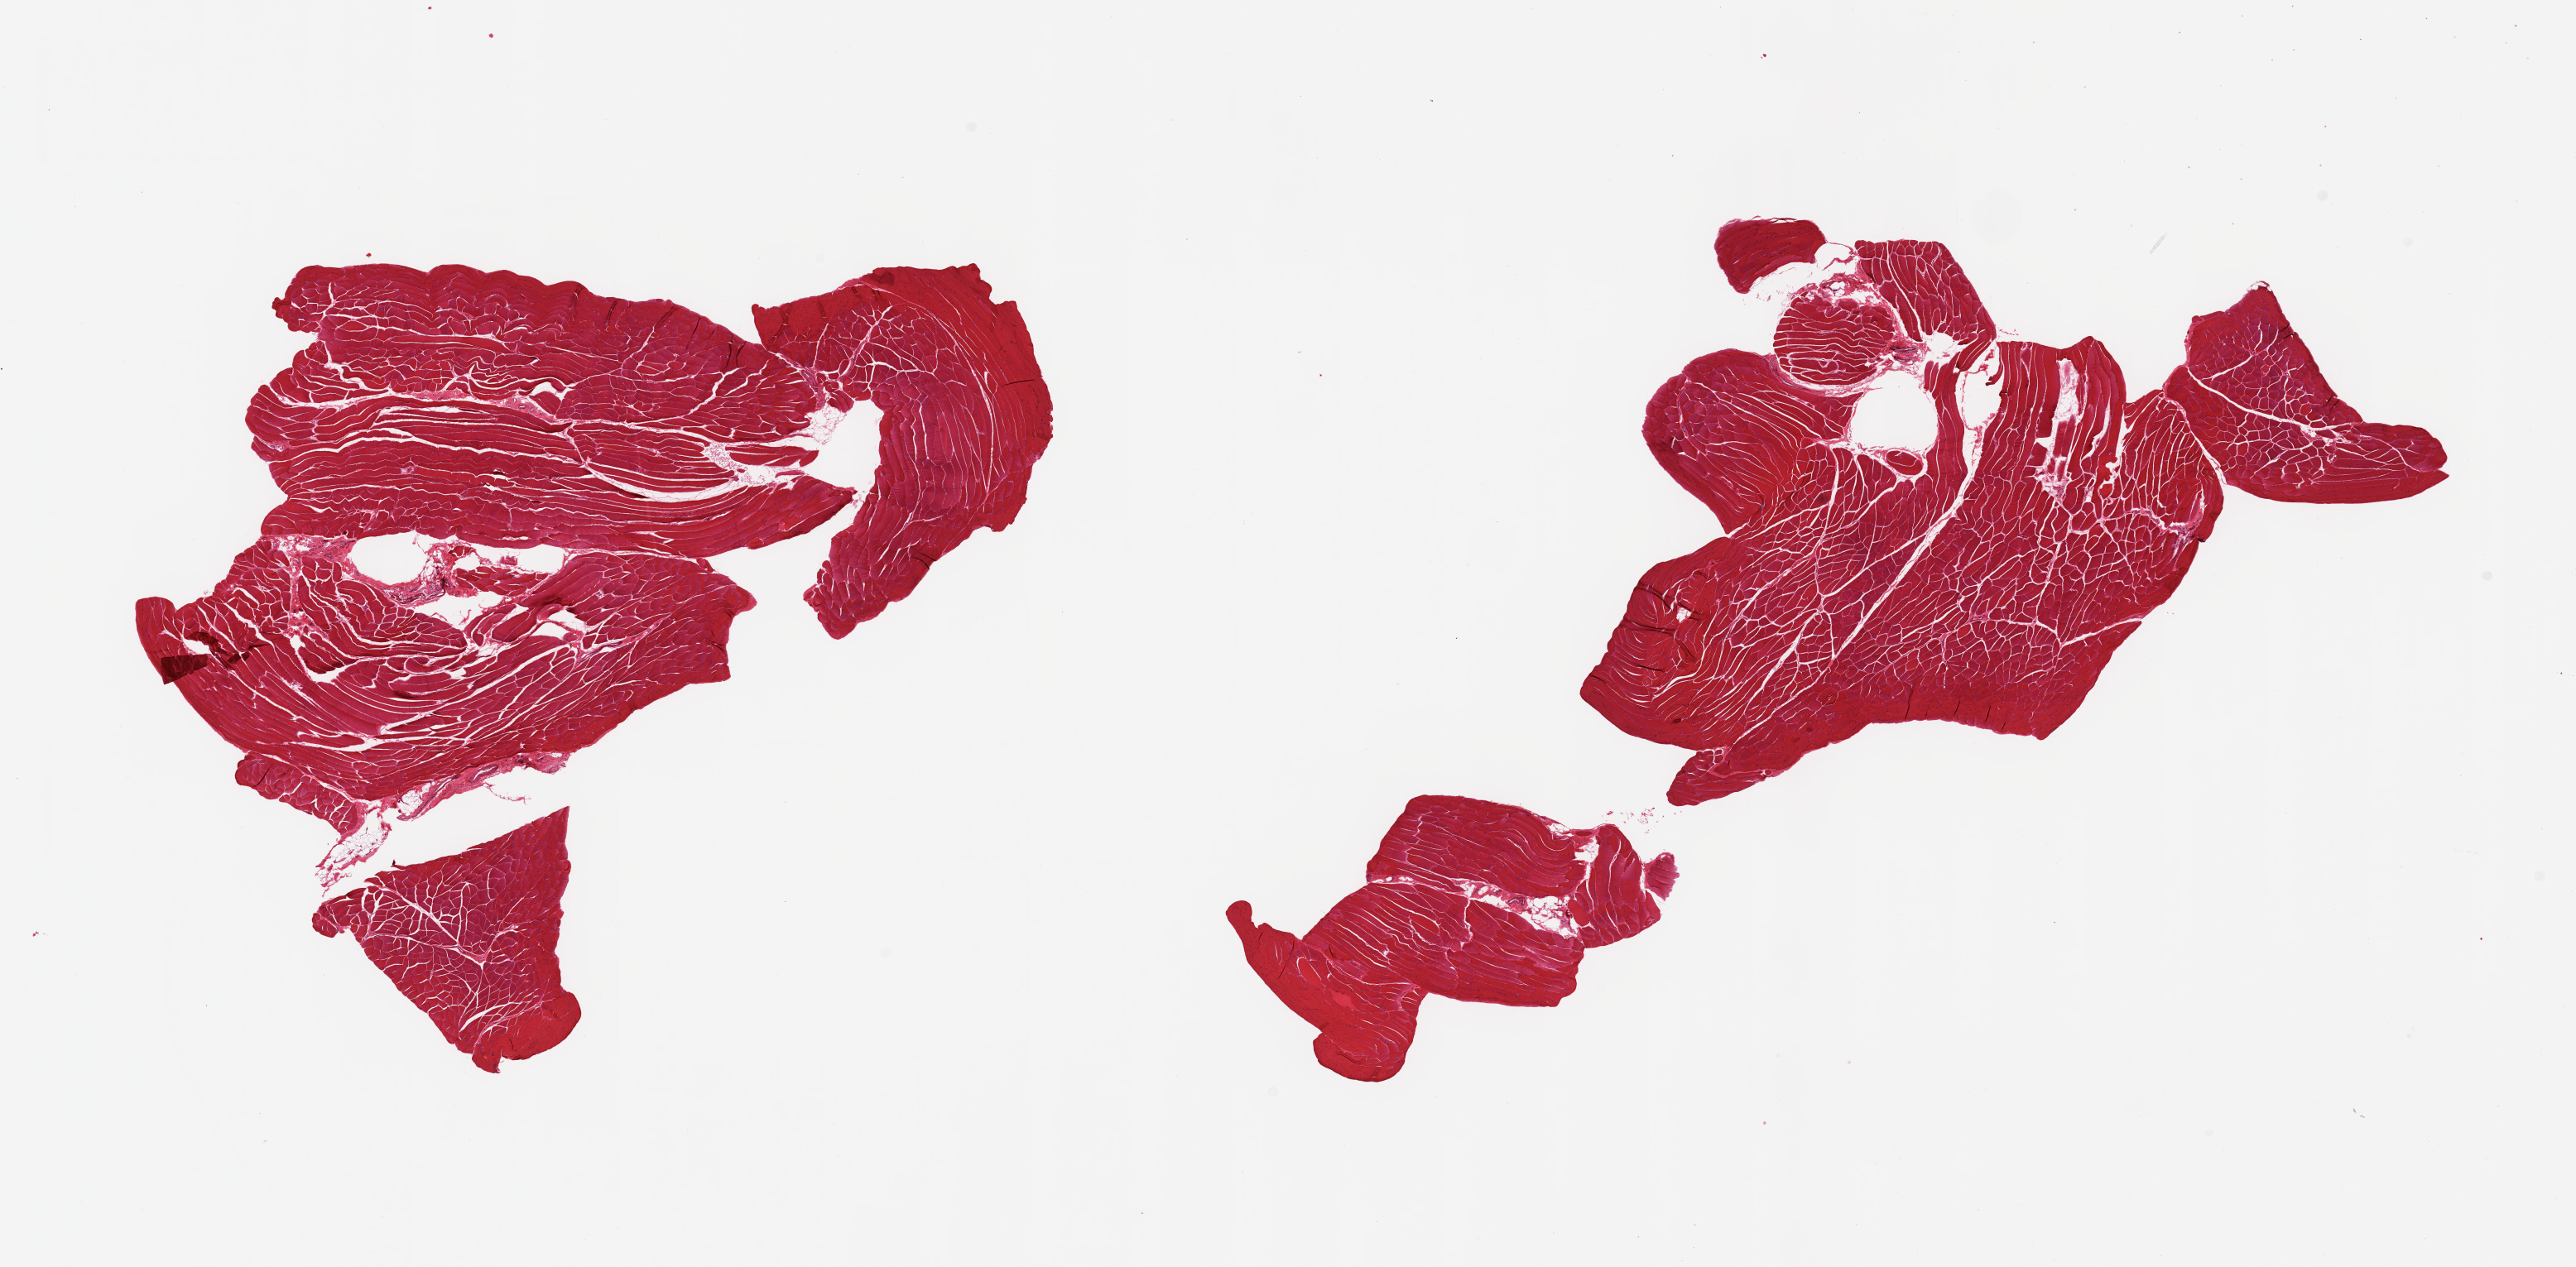
Haematoxylin and eosin whole-slide image, brightfield, shown as a low-resolution overview of the whole scanned area (about 24.6 x 12.1 mm, slide scanned at 20x); PAXgene-fixed paraffin-embedded (PFPE) section; sampled site (target tissue): skeletal muscle; donor tissue sample.
Pathologist's review note for this sample: 2 pieces; skeletal muscle with scant internal fat, rare atrophic fiber.